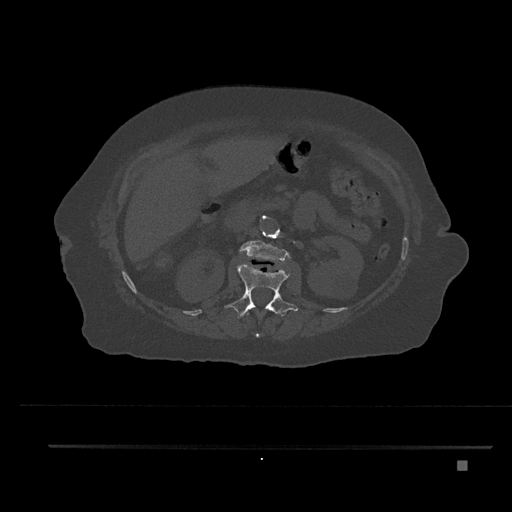
CT including the spine, one axial slice. Slice 217 of 797 in the series (ordered by position). 120 kVp. Bone window (W 1800 / L 400 HU). 0.5 mm slice thickness. 512 × 512 image matrix. Female patient, age 76 years. From the clinical record (not read from this slice): primary cancer: lung; vertebrae with lytic lesions (as recorded): T11, L3.
Outlined on this slice (semi-automatically segmented with operator editing):
- L1 vertebra: bounding box <225,263,298,319> (left, top, right, bottom; pixels)
- L2 vertebra: <240,240,289,261>
- T12 vertebra: <245,311,275,338>